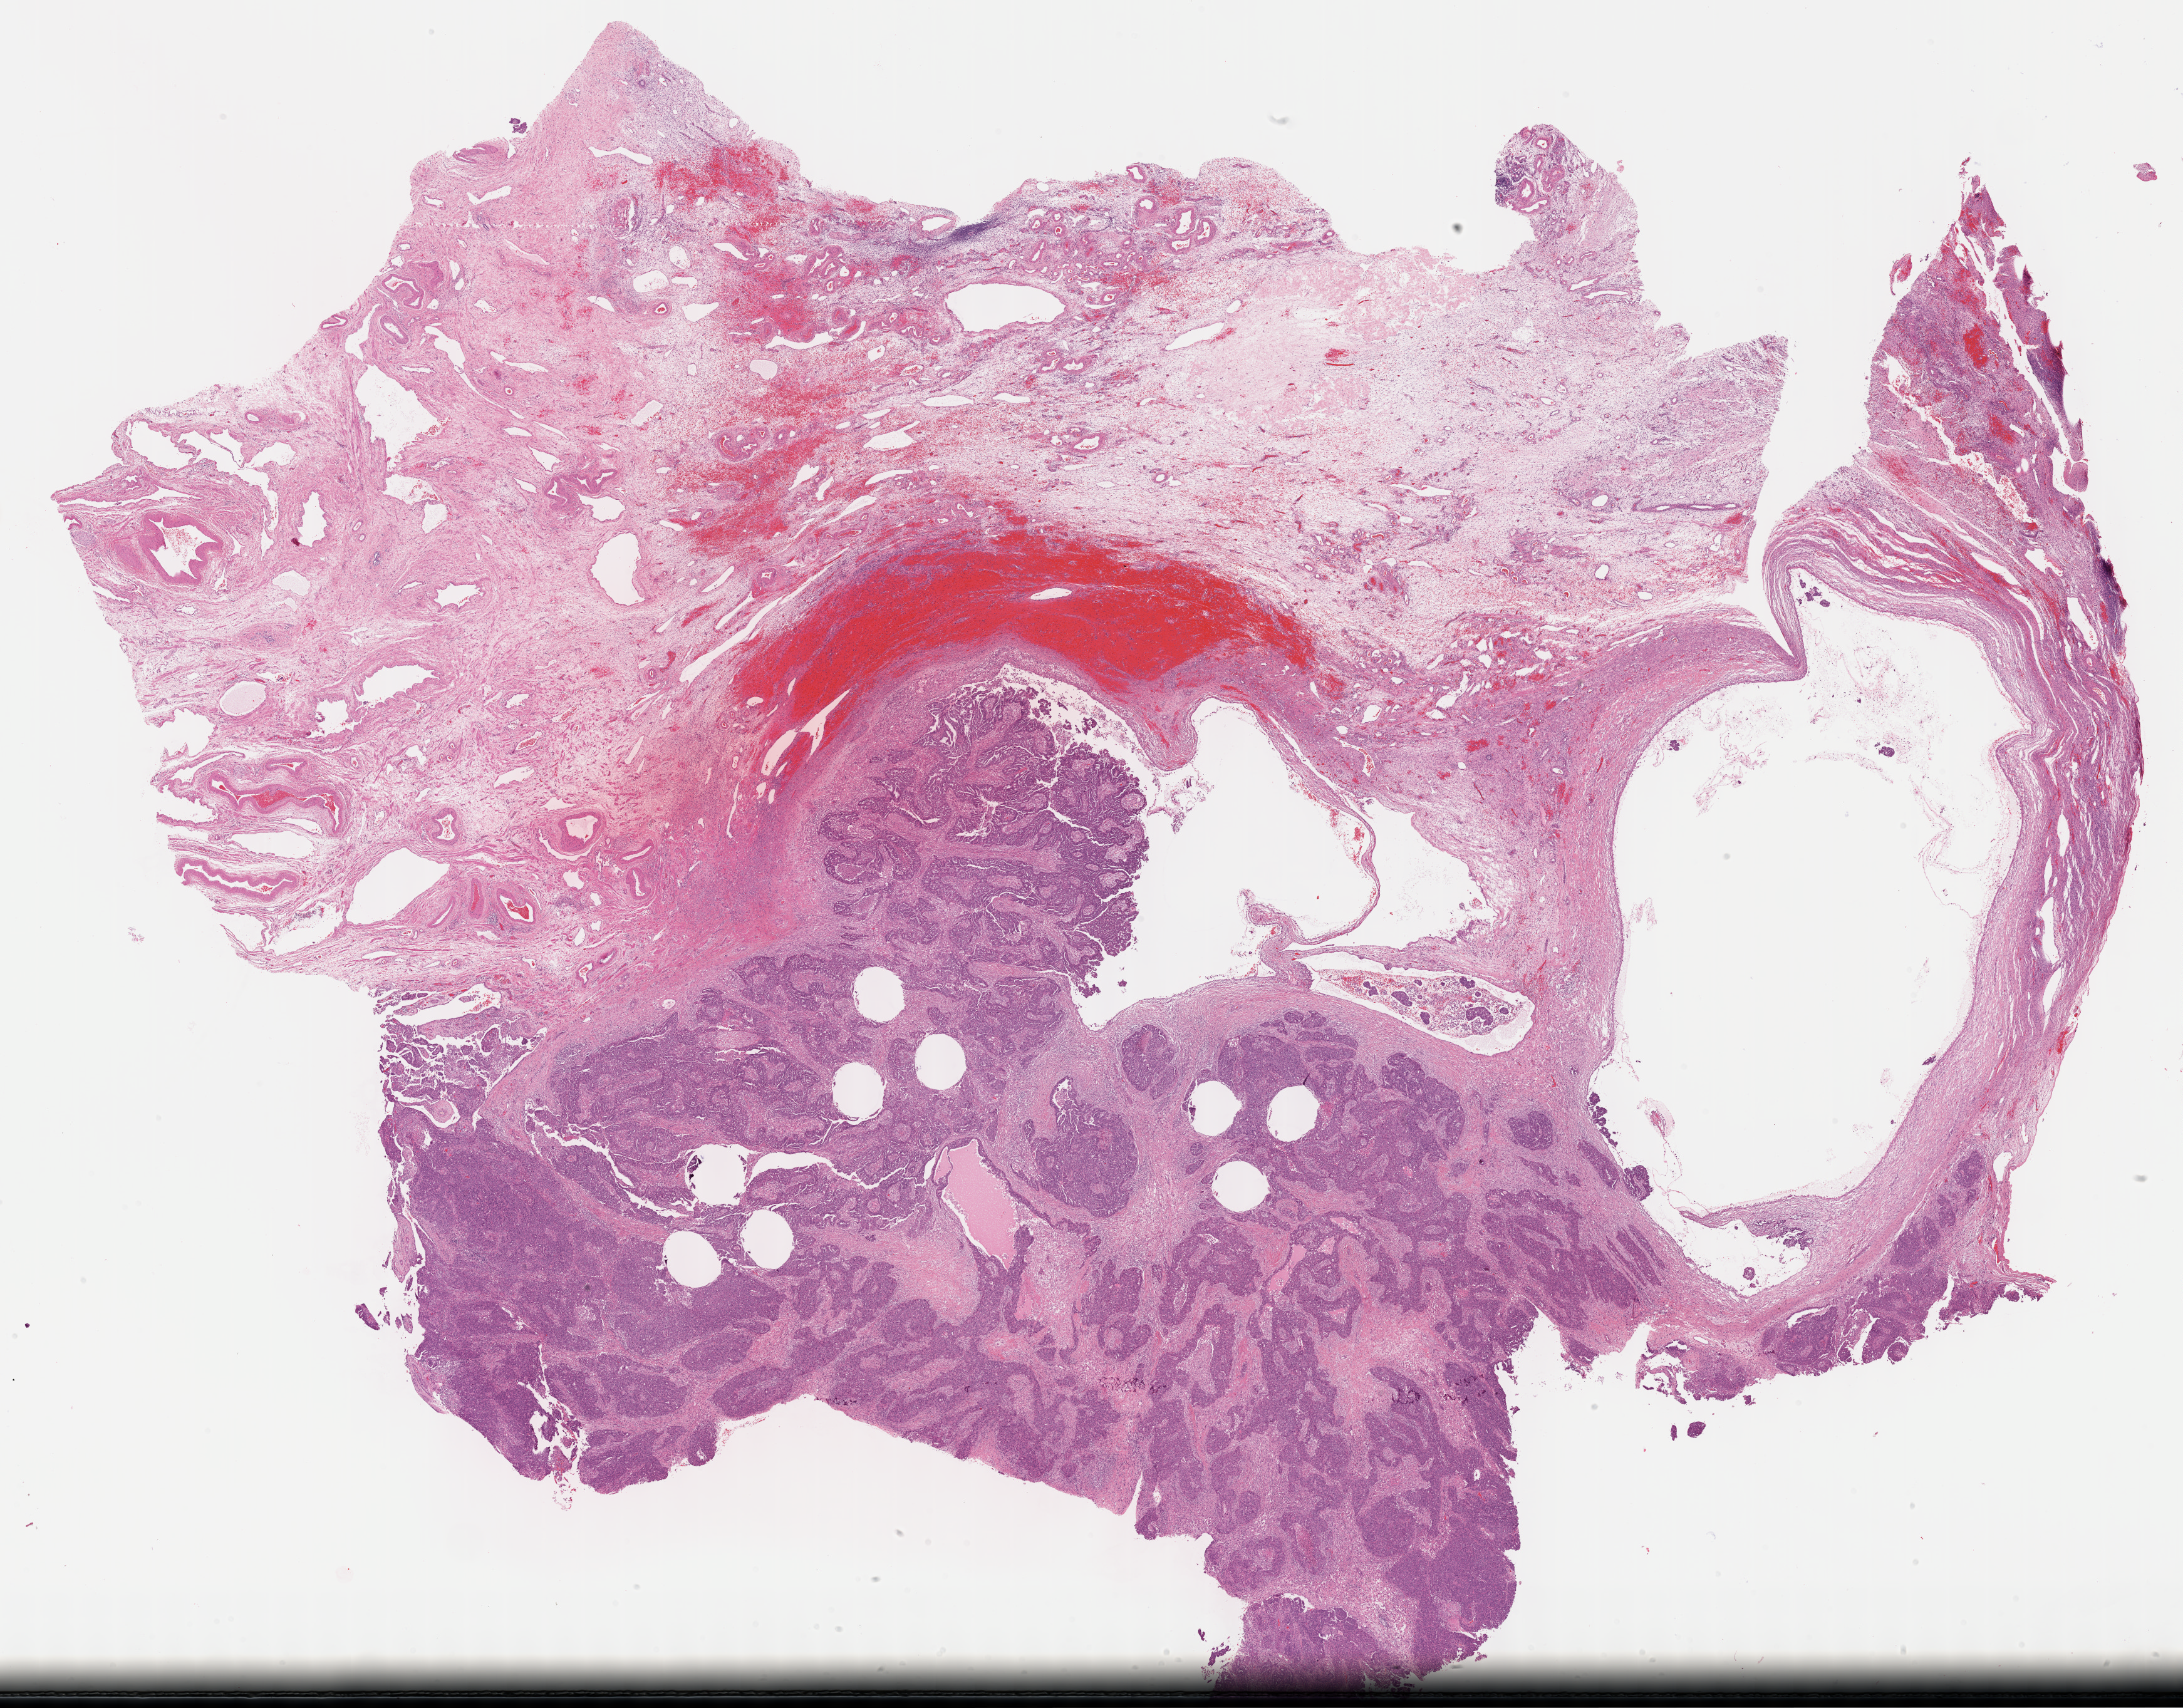
Whole-slide histology image, H&E-stained, low-resolution overview of the scanned area, about 28.2 x 22.1 mm (slide scanned at 40x). FFPE section. Sample: primary tumour, ovary. Female patient; age at initial diagnosis 45 years.
Histologic diagnosis: Serous cystadenocarcinoma, NOS.